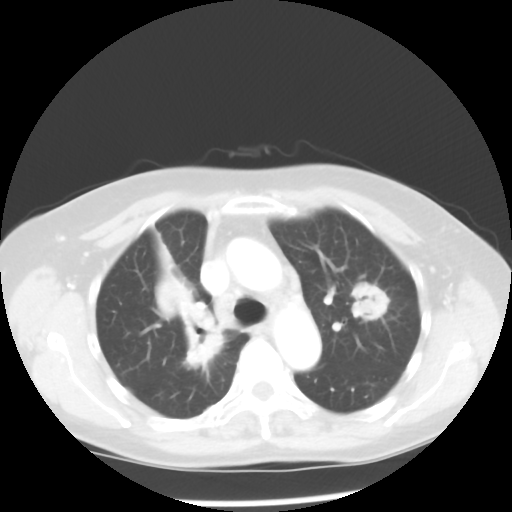
Chest CT, one axial slice. Slice 35 of 52 in the series (ordered by position). Reconstruction kernel STANDARD. Lung window (W 1500 / L -600 HU). 5 mm slice thickness. 512 × 512 image matrix, field of view 328 × 328 mm. Female patient, age 60 years. From the clinical record (not read from this slice): clinical TNM (as recorded): T2 N1 M1a.
Outlined on this slice (rectangle marked by the reading radiologist):
- lung tumour (recorded histology: adenocarcinoma): bounding box (x1, y1, x2, y2) in pixels: (151, 242, 227, 374)